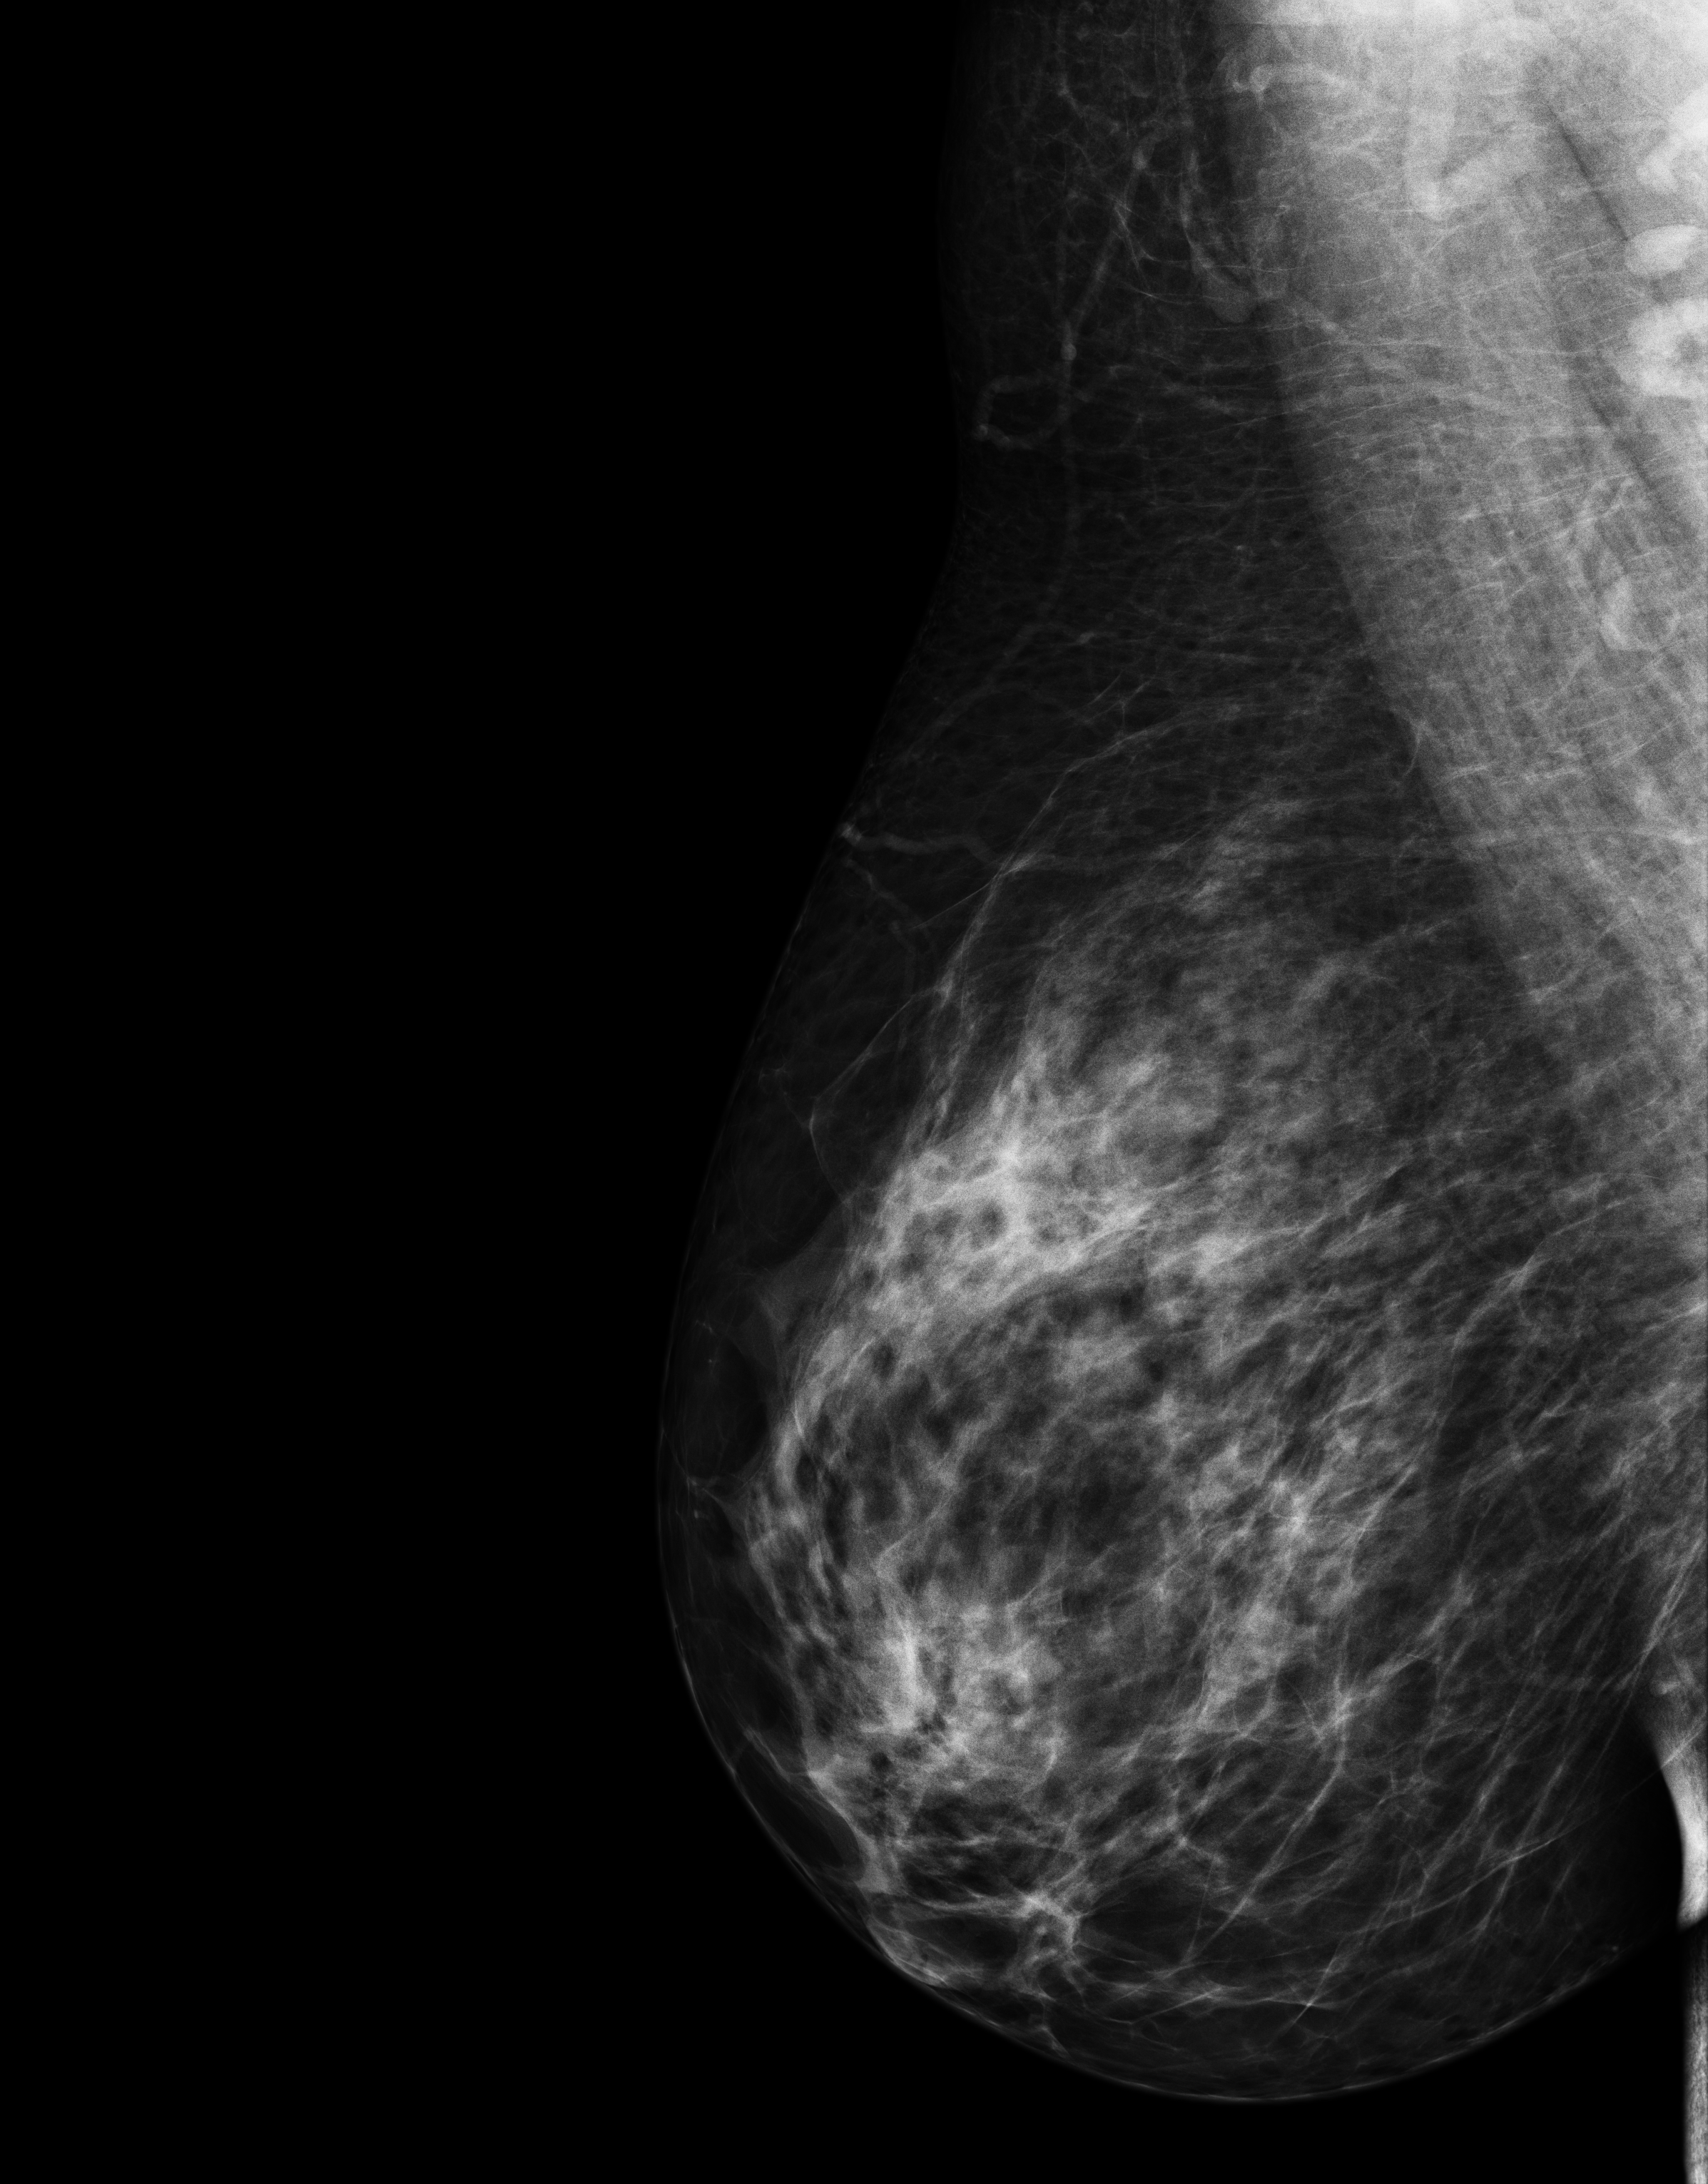
Full-field digital mammogram (FFDM); right breast; MLO view; annual screening mammography examination. Patient: female, 42 years.
Breast density at the screening exam (both breasts): heterogeneously dense (BI-RADS density category c). Final BI-RADS category for the screening round (tomosynthesis exam, both breasts): category 1. Recall: no recall after this screen.